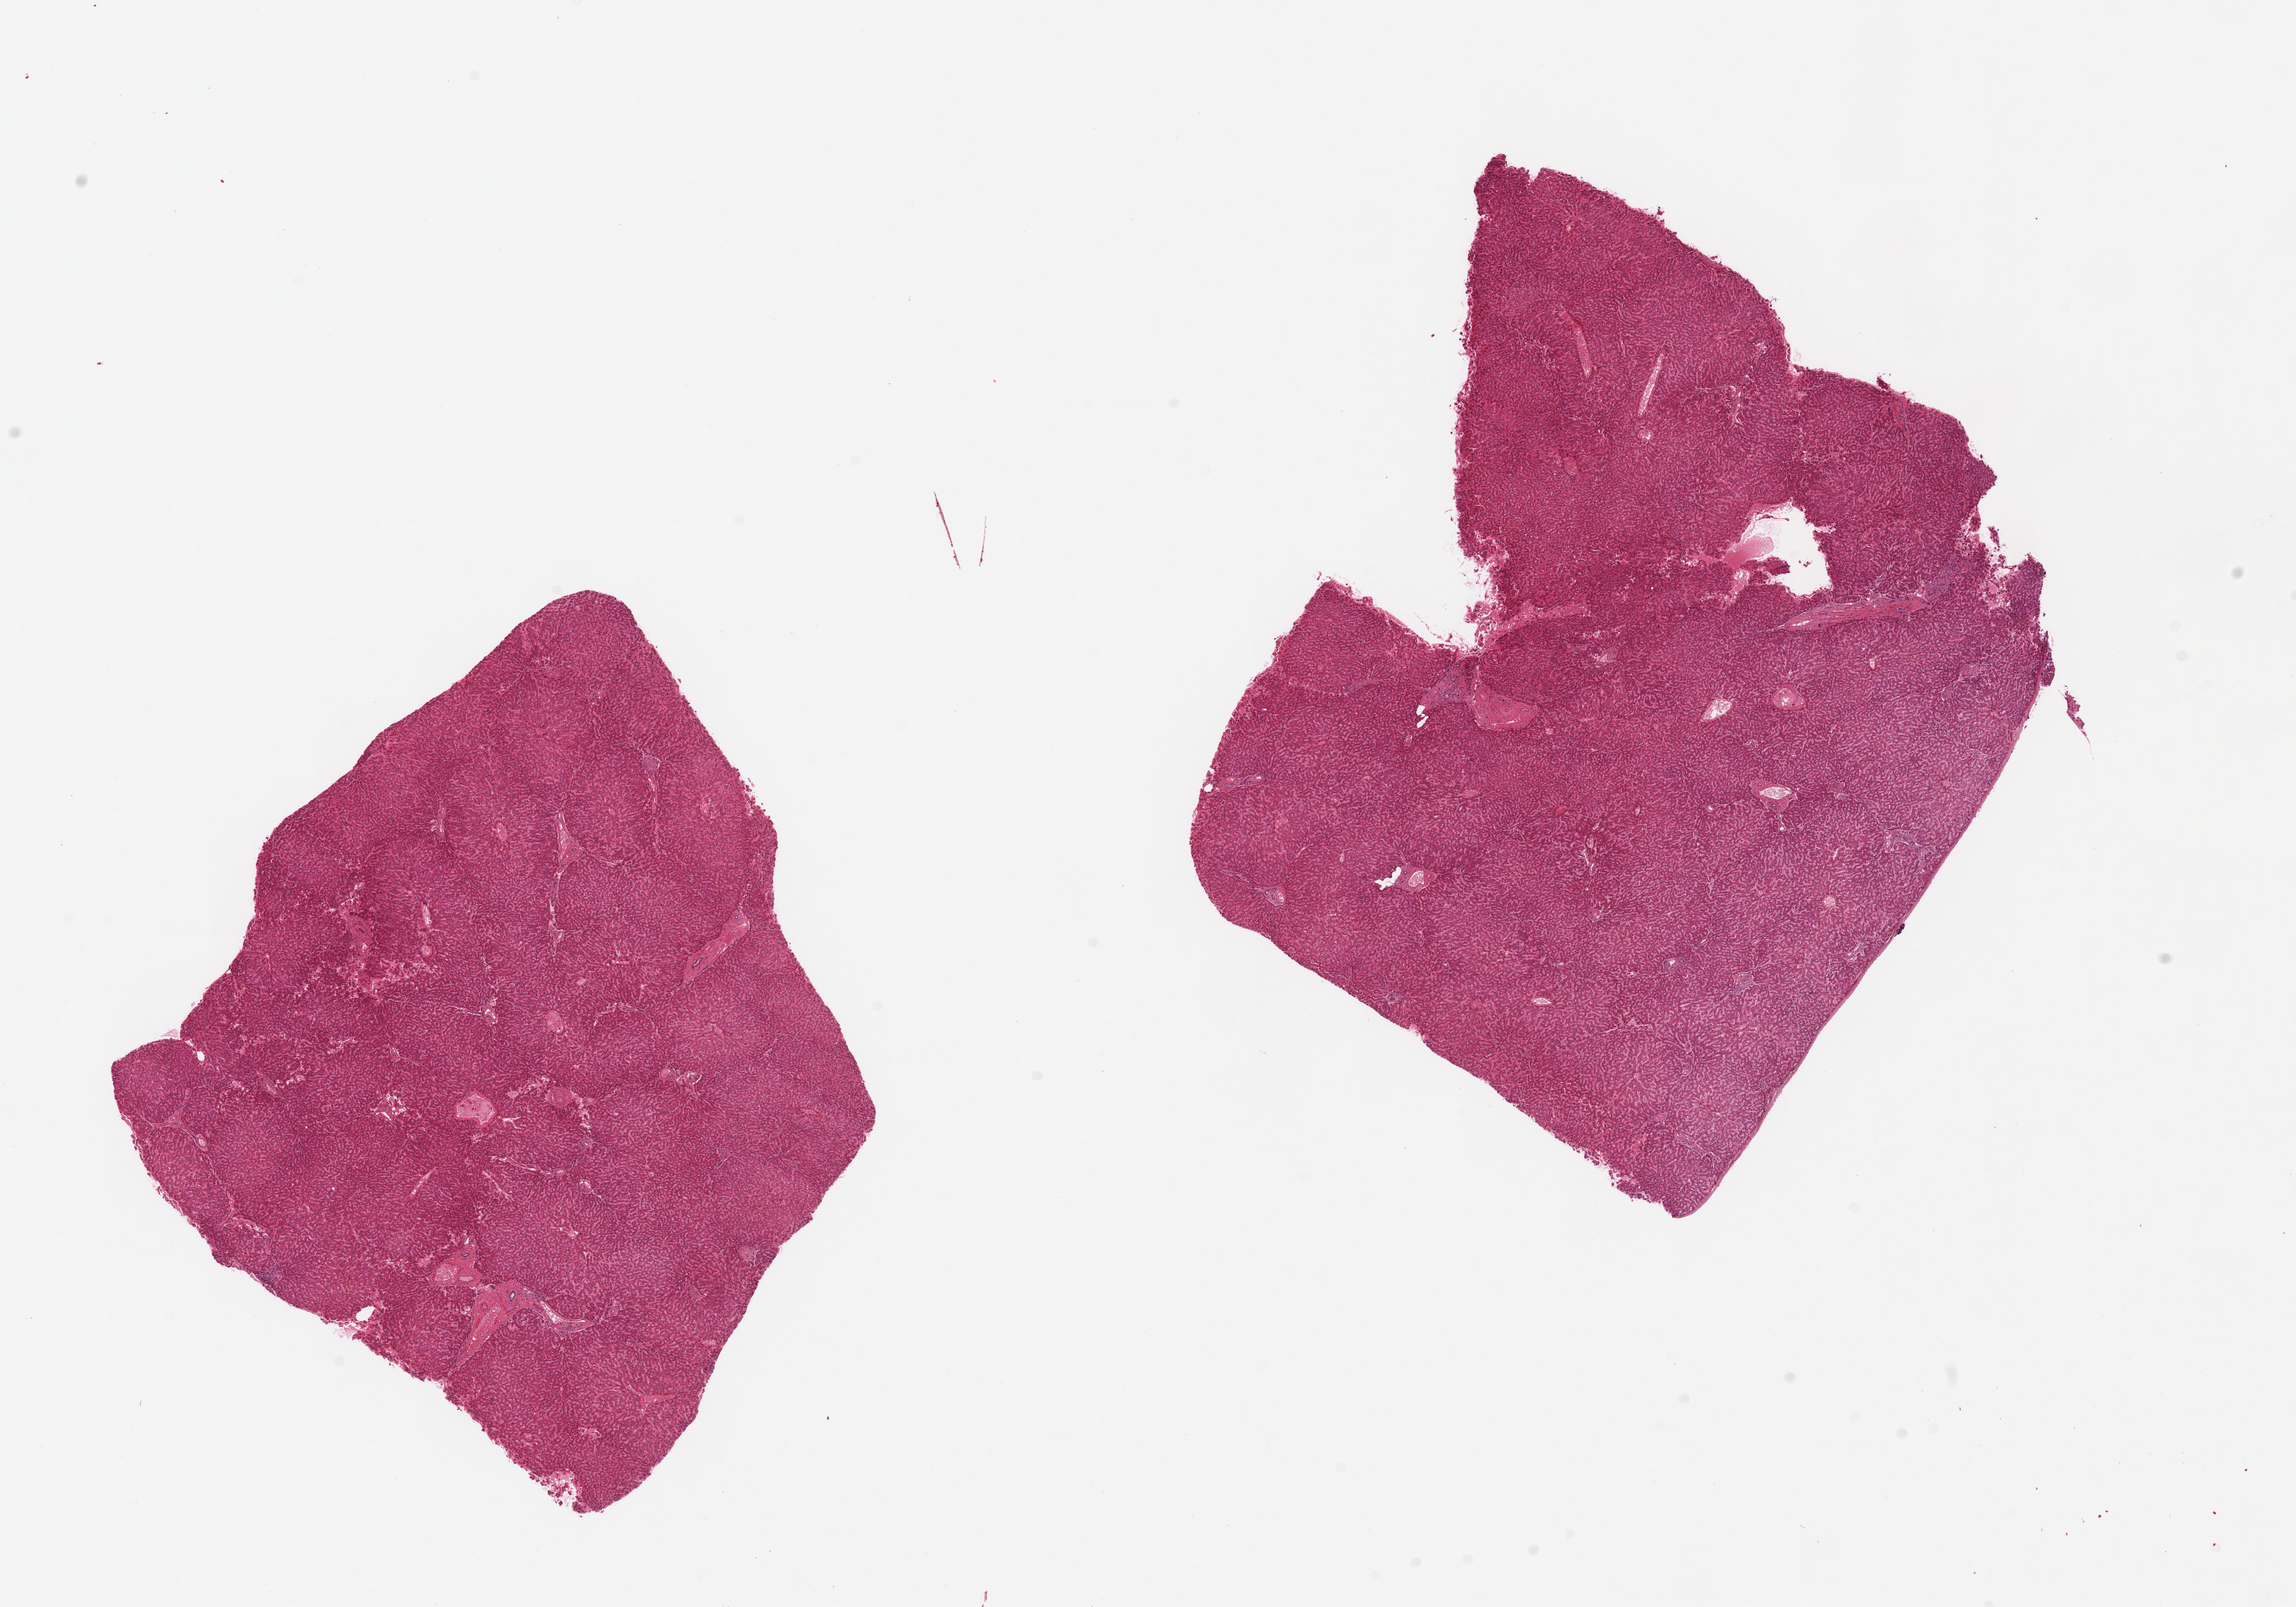
Digitized haematoxylin and eosin-stained section — low-resolution overview of the scanned area, about 21.7 x 15.2 mm (slide scanned at 20x). PAXgene-fixed, paraffin-embedded tissue. Section of liver (target tissue). Donor tissue sample. Female donor.
Reviewer comment on this tissue sample: 2 pieces, 7x7 & 8x8mm; no lesions.